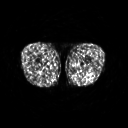
FDG PET of an extremity soft-tissue mass (from a PET/CT study), one axial slice; slice 214 of 267 in the series (ordered by position); 3.27 mm slice thickness; 128 × 128 image matrix. Male patient, age 27 years. Case-level facts recorded for this patient, not image findings: histological type: extraskeletal osteosarcoma; grade: high; site of the primary tumour: left adductur.
Structures marked on this image (expert contour drawn on MRI and transferred to this co-registered scan by the dataset authors):
- gross tumour volume (mass): bounding box <82,63,87,67> (left, top, right, bottom; pixels)